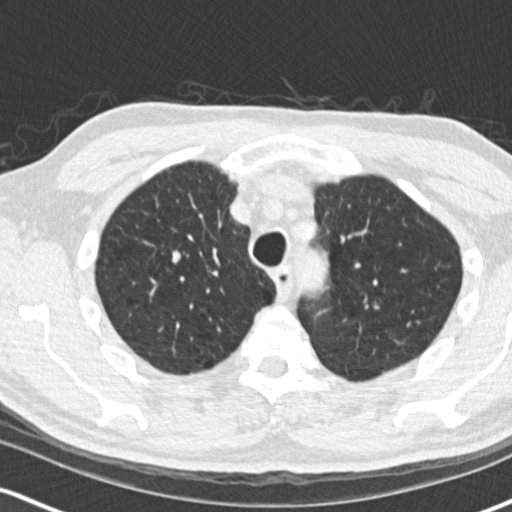
Low-dose screening chest CT, one axial slice; position 121 of 170 along the scan axis; reconstruction kernel B30f; 120 kVp; lung window (W 1500 / L -600 HU); 2 mm slice thickness; 512 × 512 image matrix, field of view 320 × 320 mm.
Structures marked on this image (outlined manually by an expert reader):
- lesion 1 (tumor, upper lobe of right lung): box from (x=172, y=250) to (x=181, y=264) px